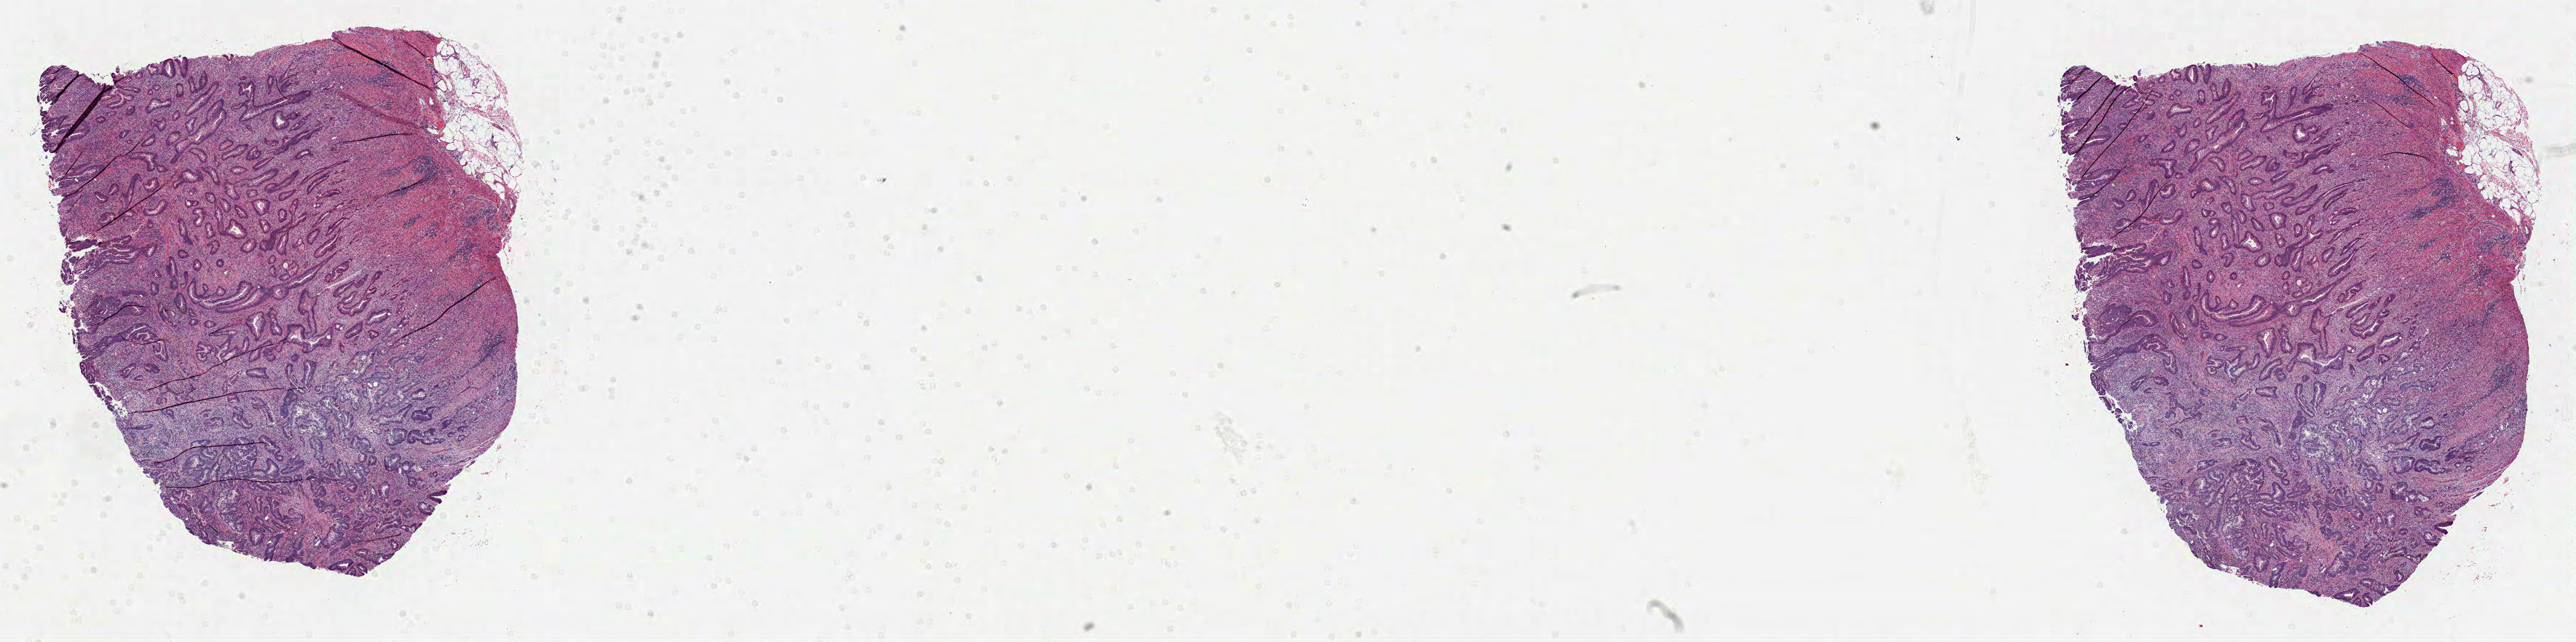
H&E-stained whole-slide image — a low-resolution overview of the entire scanned area, about 28.5 x 7.1 mm, FFPE section, sample: primary tumour, colon. Female, age 57 years at initial diagnosis.
Lymph nodes positive (case pathology): 2 of 28 examined. AJCC pathologic stage: IIIB (7th edition). Diagnosis: Adenocarcinoma, NOS (ascending colon).